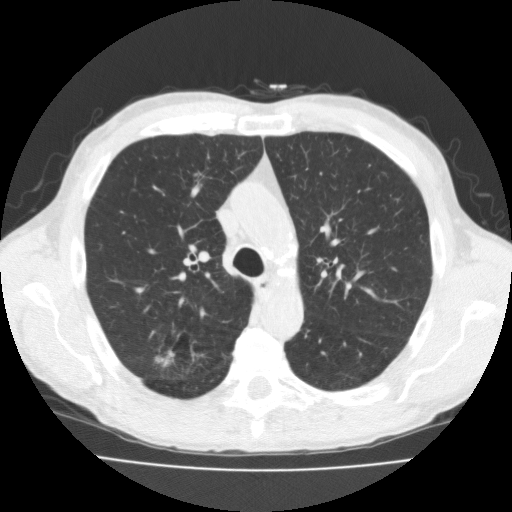
Low-dose screening chest CT, one axial slice; position 124 of 181 along the scan axis; reconstruction kernel FC10; lung window (W 1500 / L -600 HU); 512 × 512 image matrix.
Structures marked on this image (manually delineated by an expert):
- lesion 1 (tumor, upper lobe of right lung): bounding box <154,350,175,367> (left, top, right, bottom; pixels)